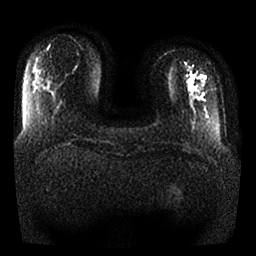
Breast MRI, one axial slice; slice 6 of 25 in the series (ordered by position); diffusion-weighted series; image 2 of 4 stored at this slice position (different b-values; order by instance number); 1.5 T; 4 mm slice thickness; 256 × 256 image matrix, field of view 340 × 340 mm. Female patient.
Structures marked on this image (outlined manually by an expert reader):
- tumour on diffusion-weighted imaging: bounding box [x1, y1, x2, y2] px = [189, 81, 193, 90]